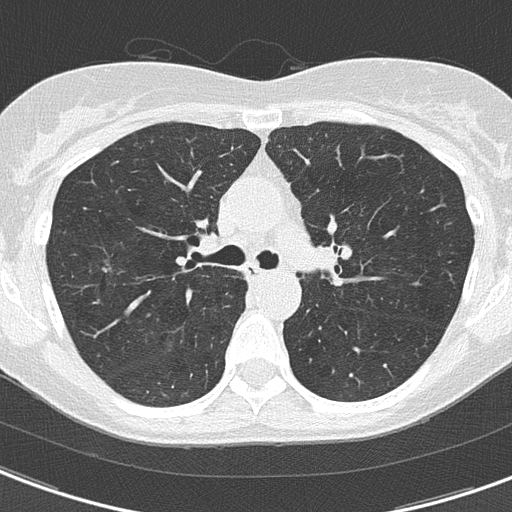
Axial slice from a low-dose chest CT screening exam. Second screening round (one year after baseline). Lung window (W 1500 / L -600 HU). 2 mm slice thickness. Lung (sharp) reconstruction kernel (B50f). Slice 55 of 156 in the series. Female, age 59 years at enrolment. Current smoker at enrolment.
Lesion marked by an expert reader, bounding box (x1, y1, x2, y2) in pixels: (87, 249, 137, 288). Reader record for this screening exam (exam-level; its link to the box is not recorded): non-calcified nodule or mass ≥4 mm, right upper lobe, 7 × 6 mm, poorly defined margins, ground glass attenuation, pre-existing on the prior screen: yes; interval growth: no. Official screen result: positive, no significant change: stable abnormalities potentially related to lung cancer, unchanged since the prior screening exam. Later outcome: lung cancer diagnosed 454 days after this screen (after the third annual screen) — bronchiolo-alveolar adenocarcinoma, NOS, right upper lobe, well differentiated (G1), stage IA (AJCC 6th edition), 4 mm at pathology.